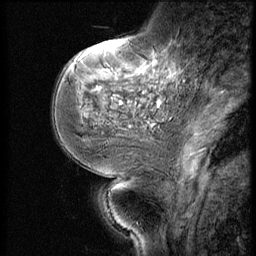
Breast MRI (dynamic contrast-enhanced), one sagittal slice; slice 20 of 56 in the series (ordered by position); dynamic contrast-enhanced series, image 2 of 3 at this slice position (ordered by acquisition); 1.5 T; TE 4.2 ms, TR 9 ms; 256 × 256 image matrix. Female patient, age 51 years. From the clinical record (not read from this slice): setting: breast cancer imaged before/during neoadjuvant chemotherapy; receptor status: triple-negative.
Annotated regions visible in this slice (semi-automatic segmentation, software-assisted and operator-edited):
- analysis volume of interest (the breast-tissue region the enhancement analysis was run in; not a lesion): bounding box (x1, y1, x2, y2) in pixels: (73, 46, 172, 147)
- tumour enhancement mask (voxels above the 140 % enhancement threshold inside the analysis volume of interest): (138, 60, 172, 107)